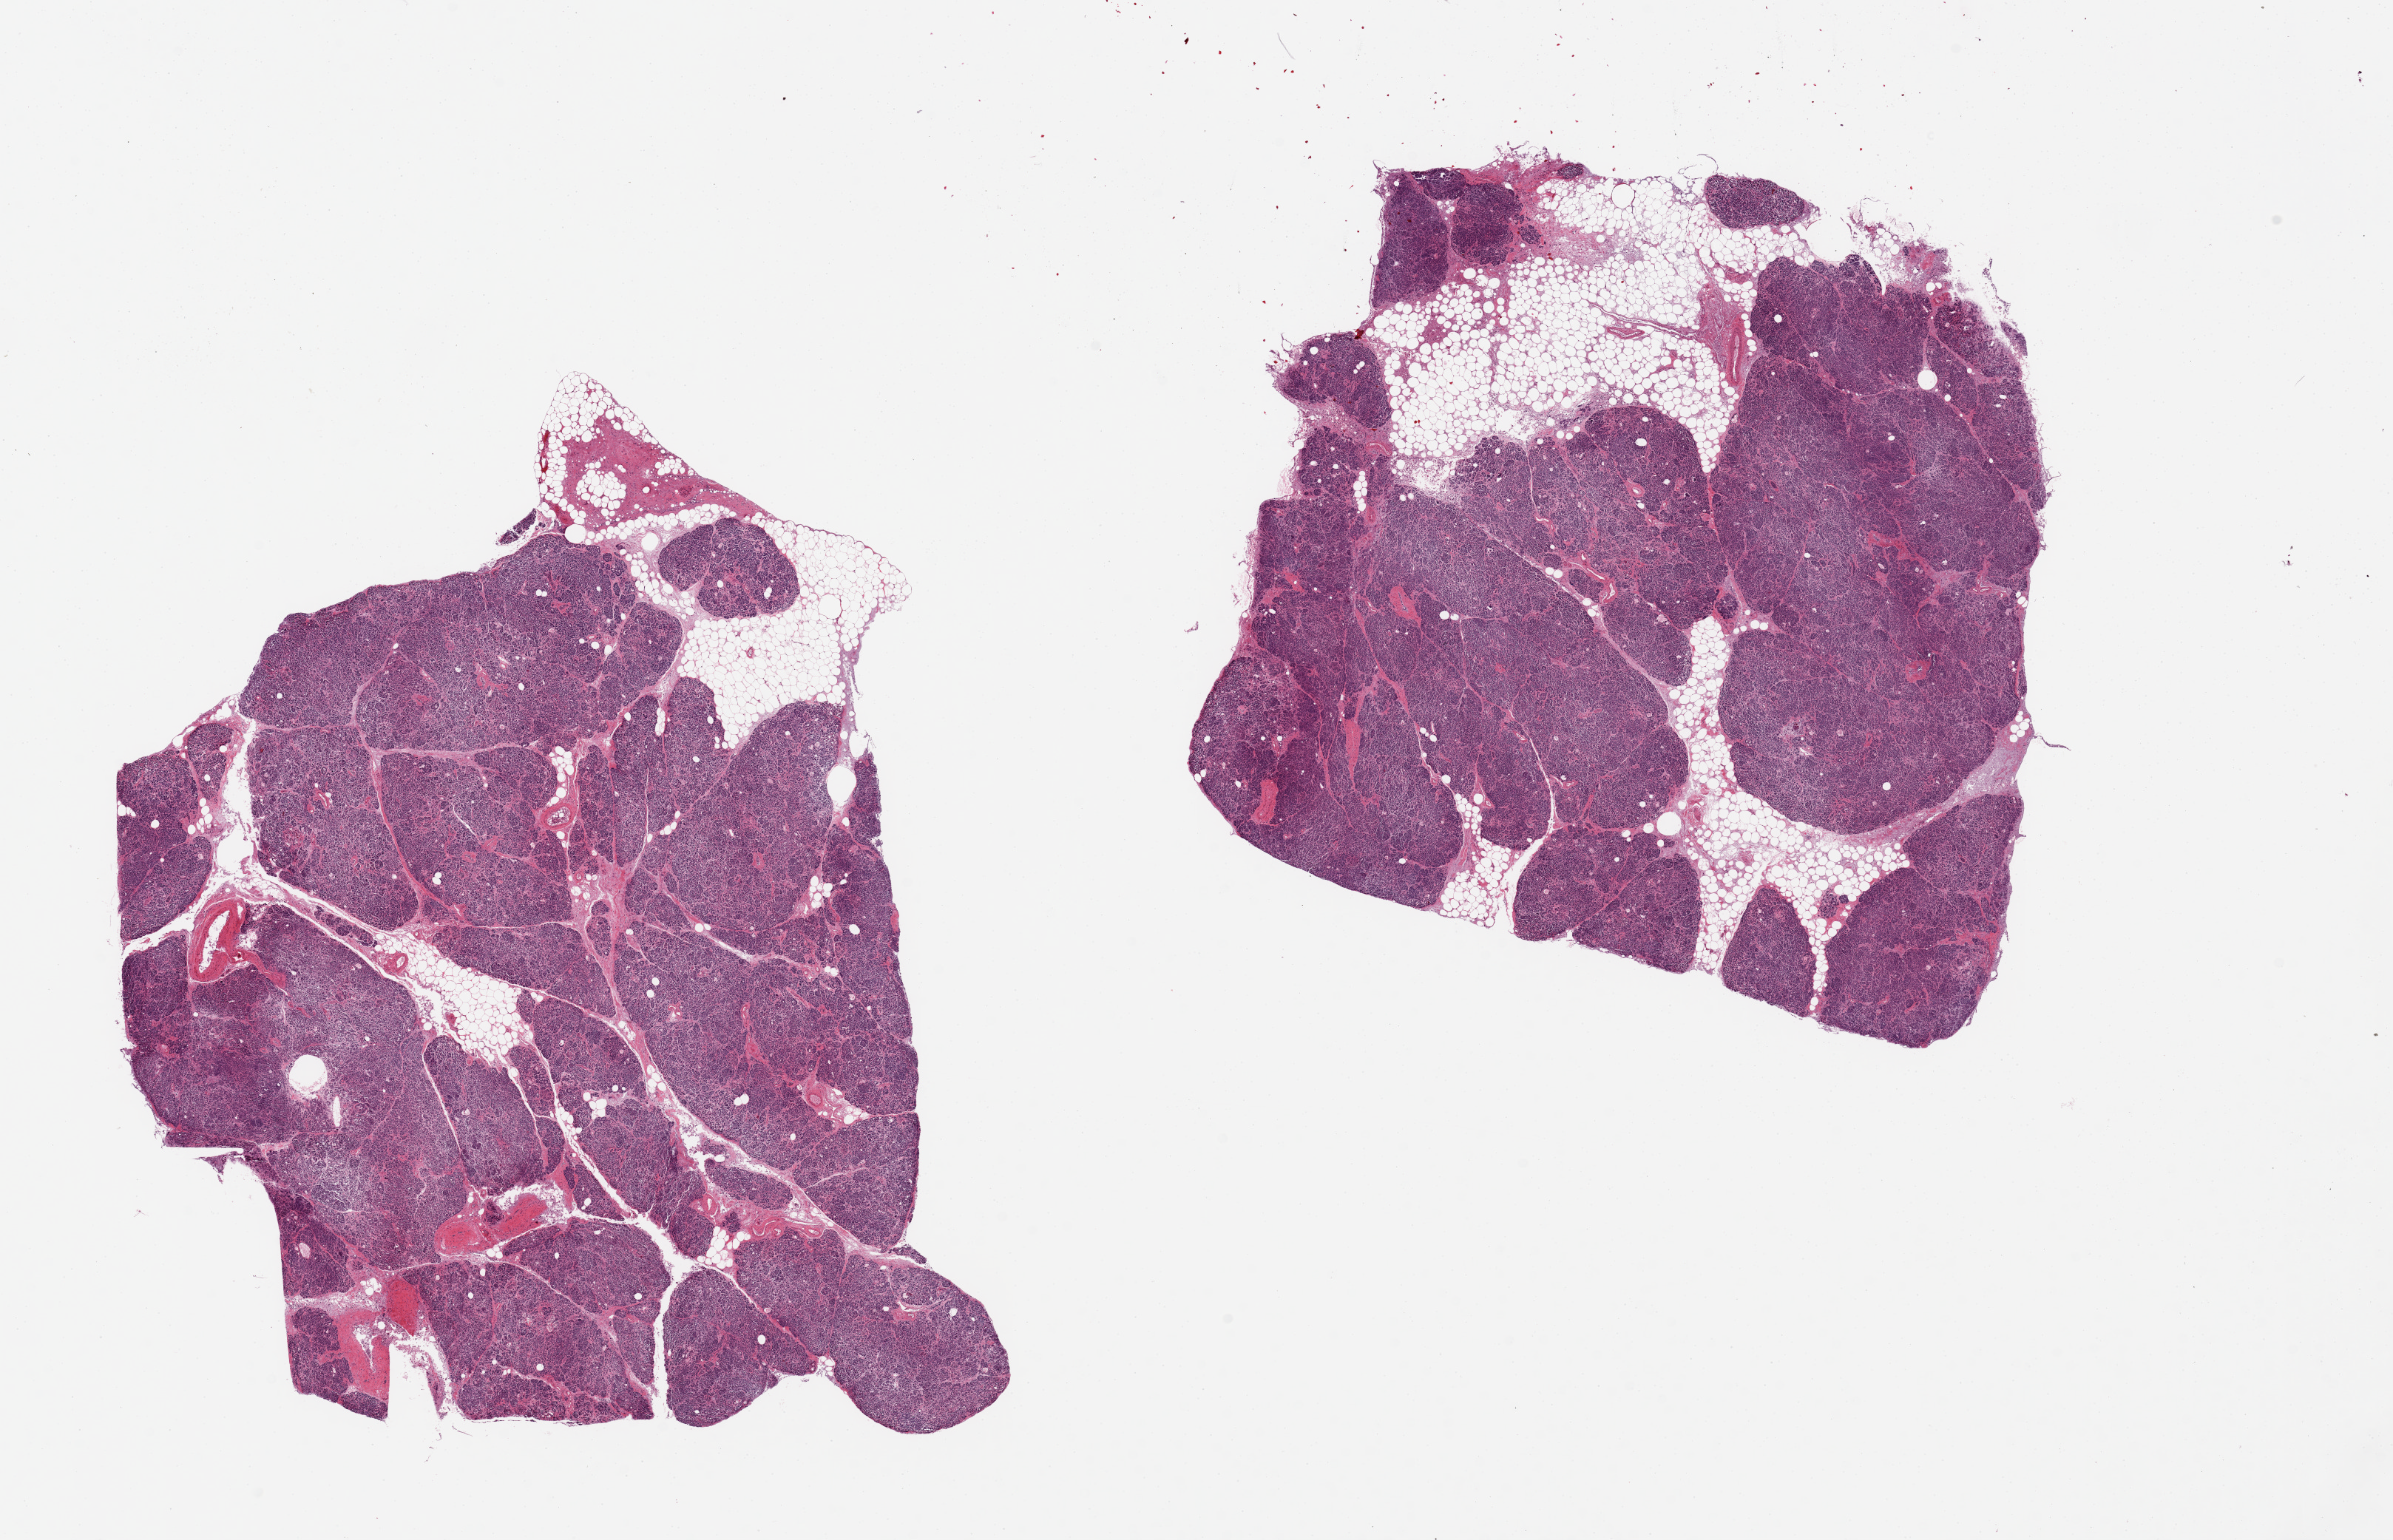
Hematoxylin and eosin (H&E) whole-slide image, brightfield, whole scanned area (about 25.6 x 16.5 mm) shown as a low-resolution overview, PAXgene-fixed paraffin-embedded (PFPE) section, target tissue: pancreas, donor tissue sample. Male donor.
- review note (as recorded): 2 pieces, marked atuolysis/saponification